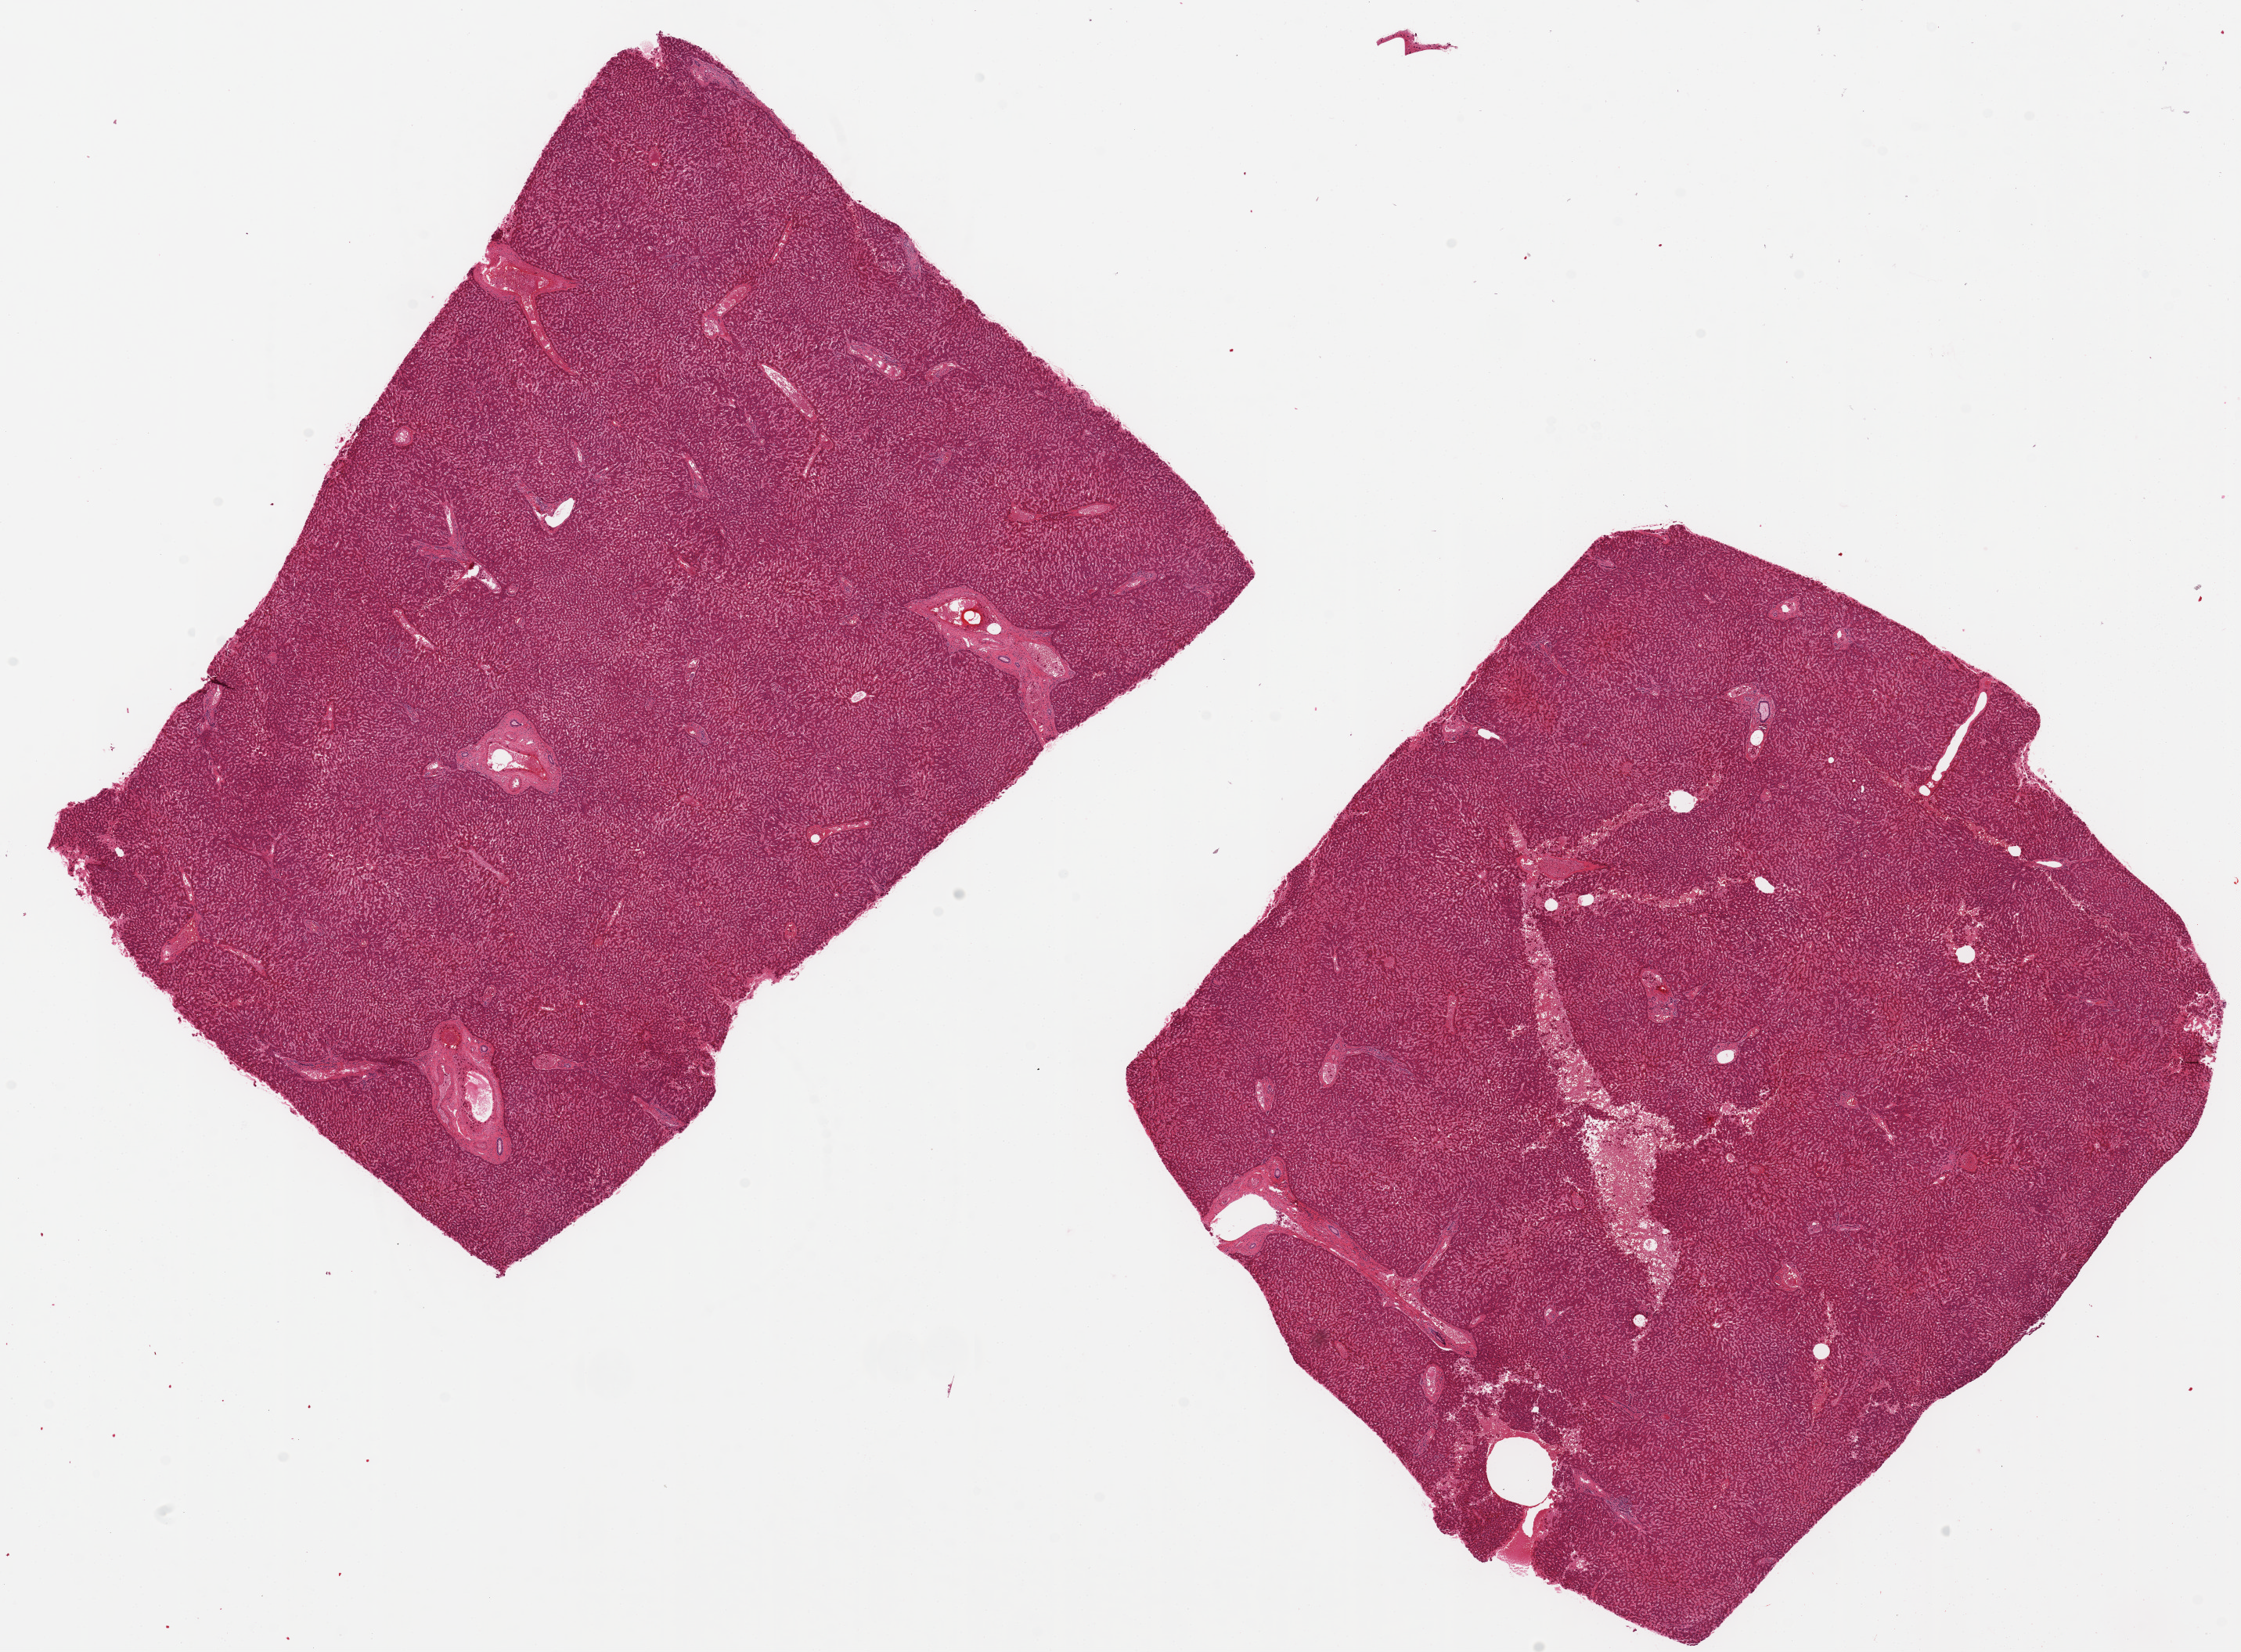
Whole-slide image, H&E stain — a low-resolution overview of the entire scanned area, about 22.6 x 16.7 mm; PAXgene-fixed, paraffin-embedded tissue; section of liver (target tissue); tissue donor sample.
Review note (as recorded): 2 ~9x8mm aliquots, areas of chronic passive congestion.